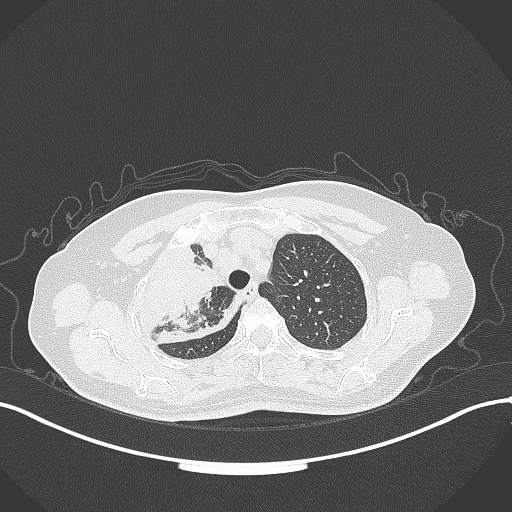
Chest CT, one axial slice; slice 252 of 309 in the series (ordered by position); reconstruction kernel B70f; 120 kVp; lung window (W 1500 / L -600 HU); 1 mm slice thickness; 512 × 512 image matrix. Patient: female, 60 years. Case-level facts recorded for this patient, not image findings: clinical TNM (as recorded): T3 N1 M1.
Annotated regions visible in this slice (bounding box drawn by a radiologist):
- lung tumour (recorded histology: adenocarcinoma): box from (x=133, y=239) to (x=245, y=351) px